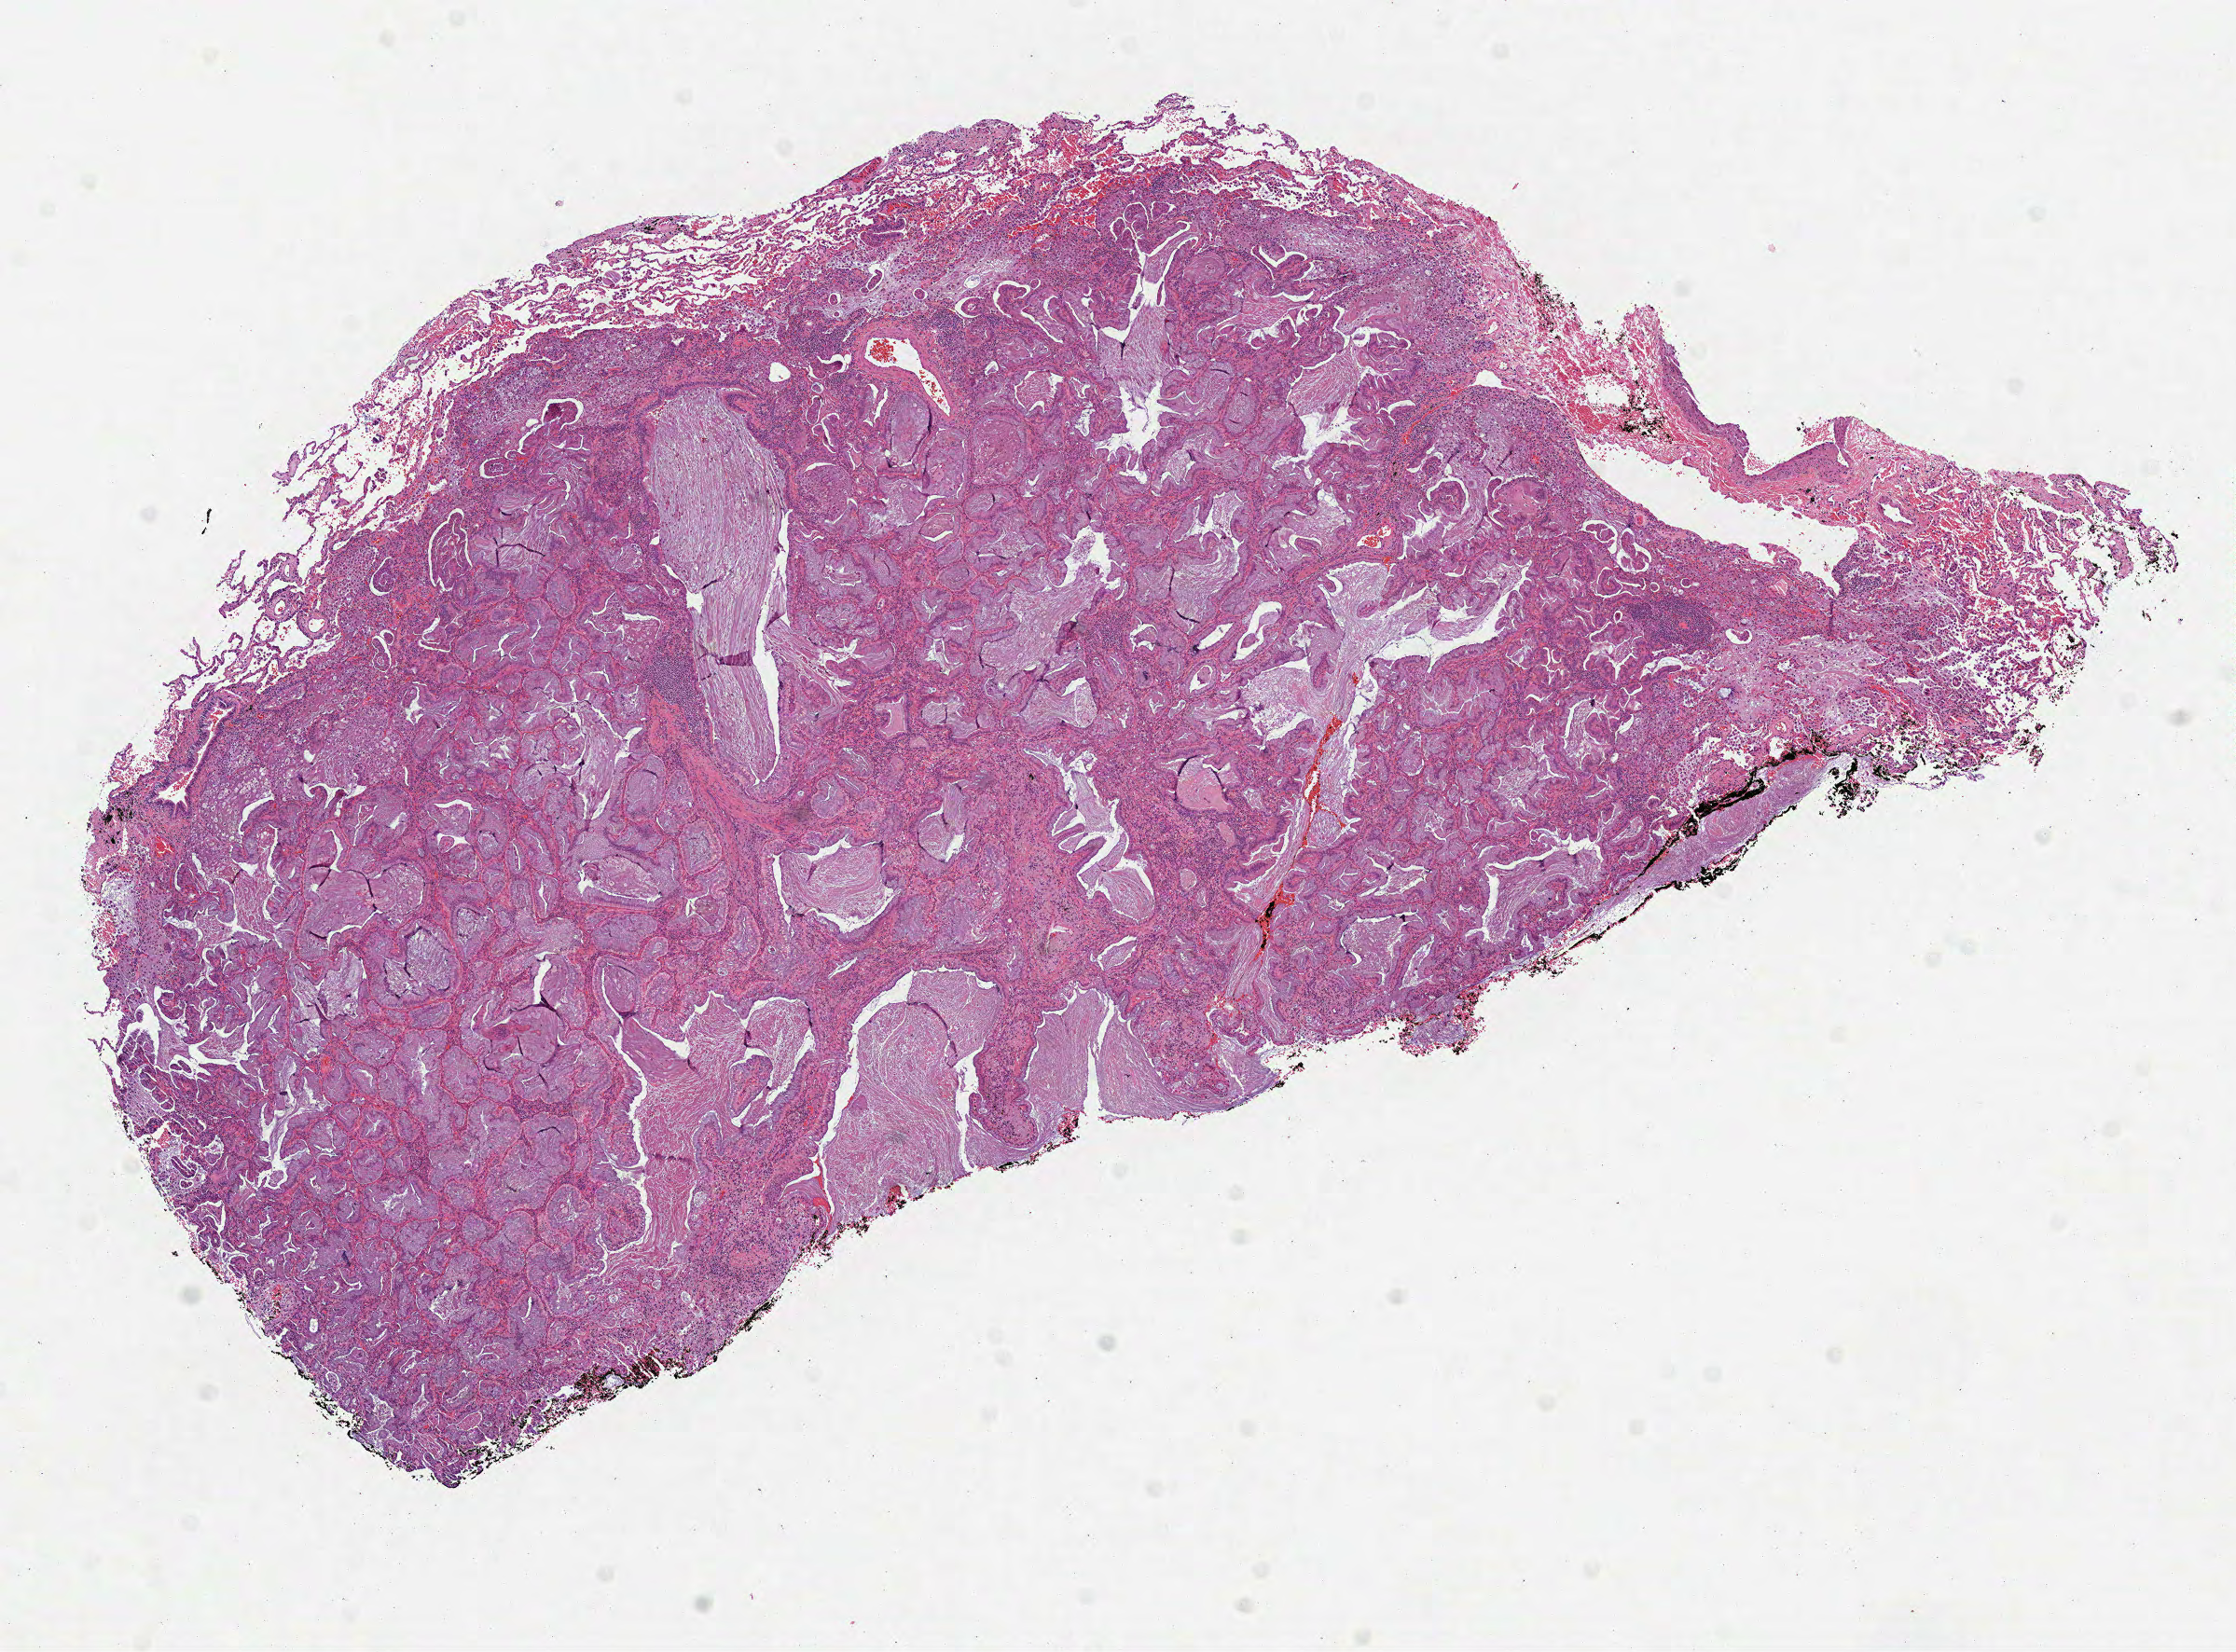
Digitized H&E tissue section (whole slide), whole scanned area (about 9.7 x 7.1 mm) shown as a low-resolution overview. FFPE section. Primary tumour sample from the lung. Patient: female, age at initial diagnosis 64 years.
* laterality: left
* pathologic diagnosis: Mucinous adenocarcinoma (upper lobe, lung)
* AJCC pathologic stage: IB (7th edition)
* TNM: T2a N0 MX